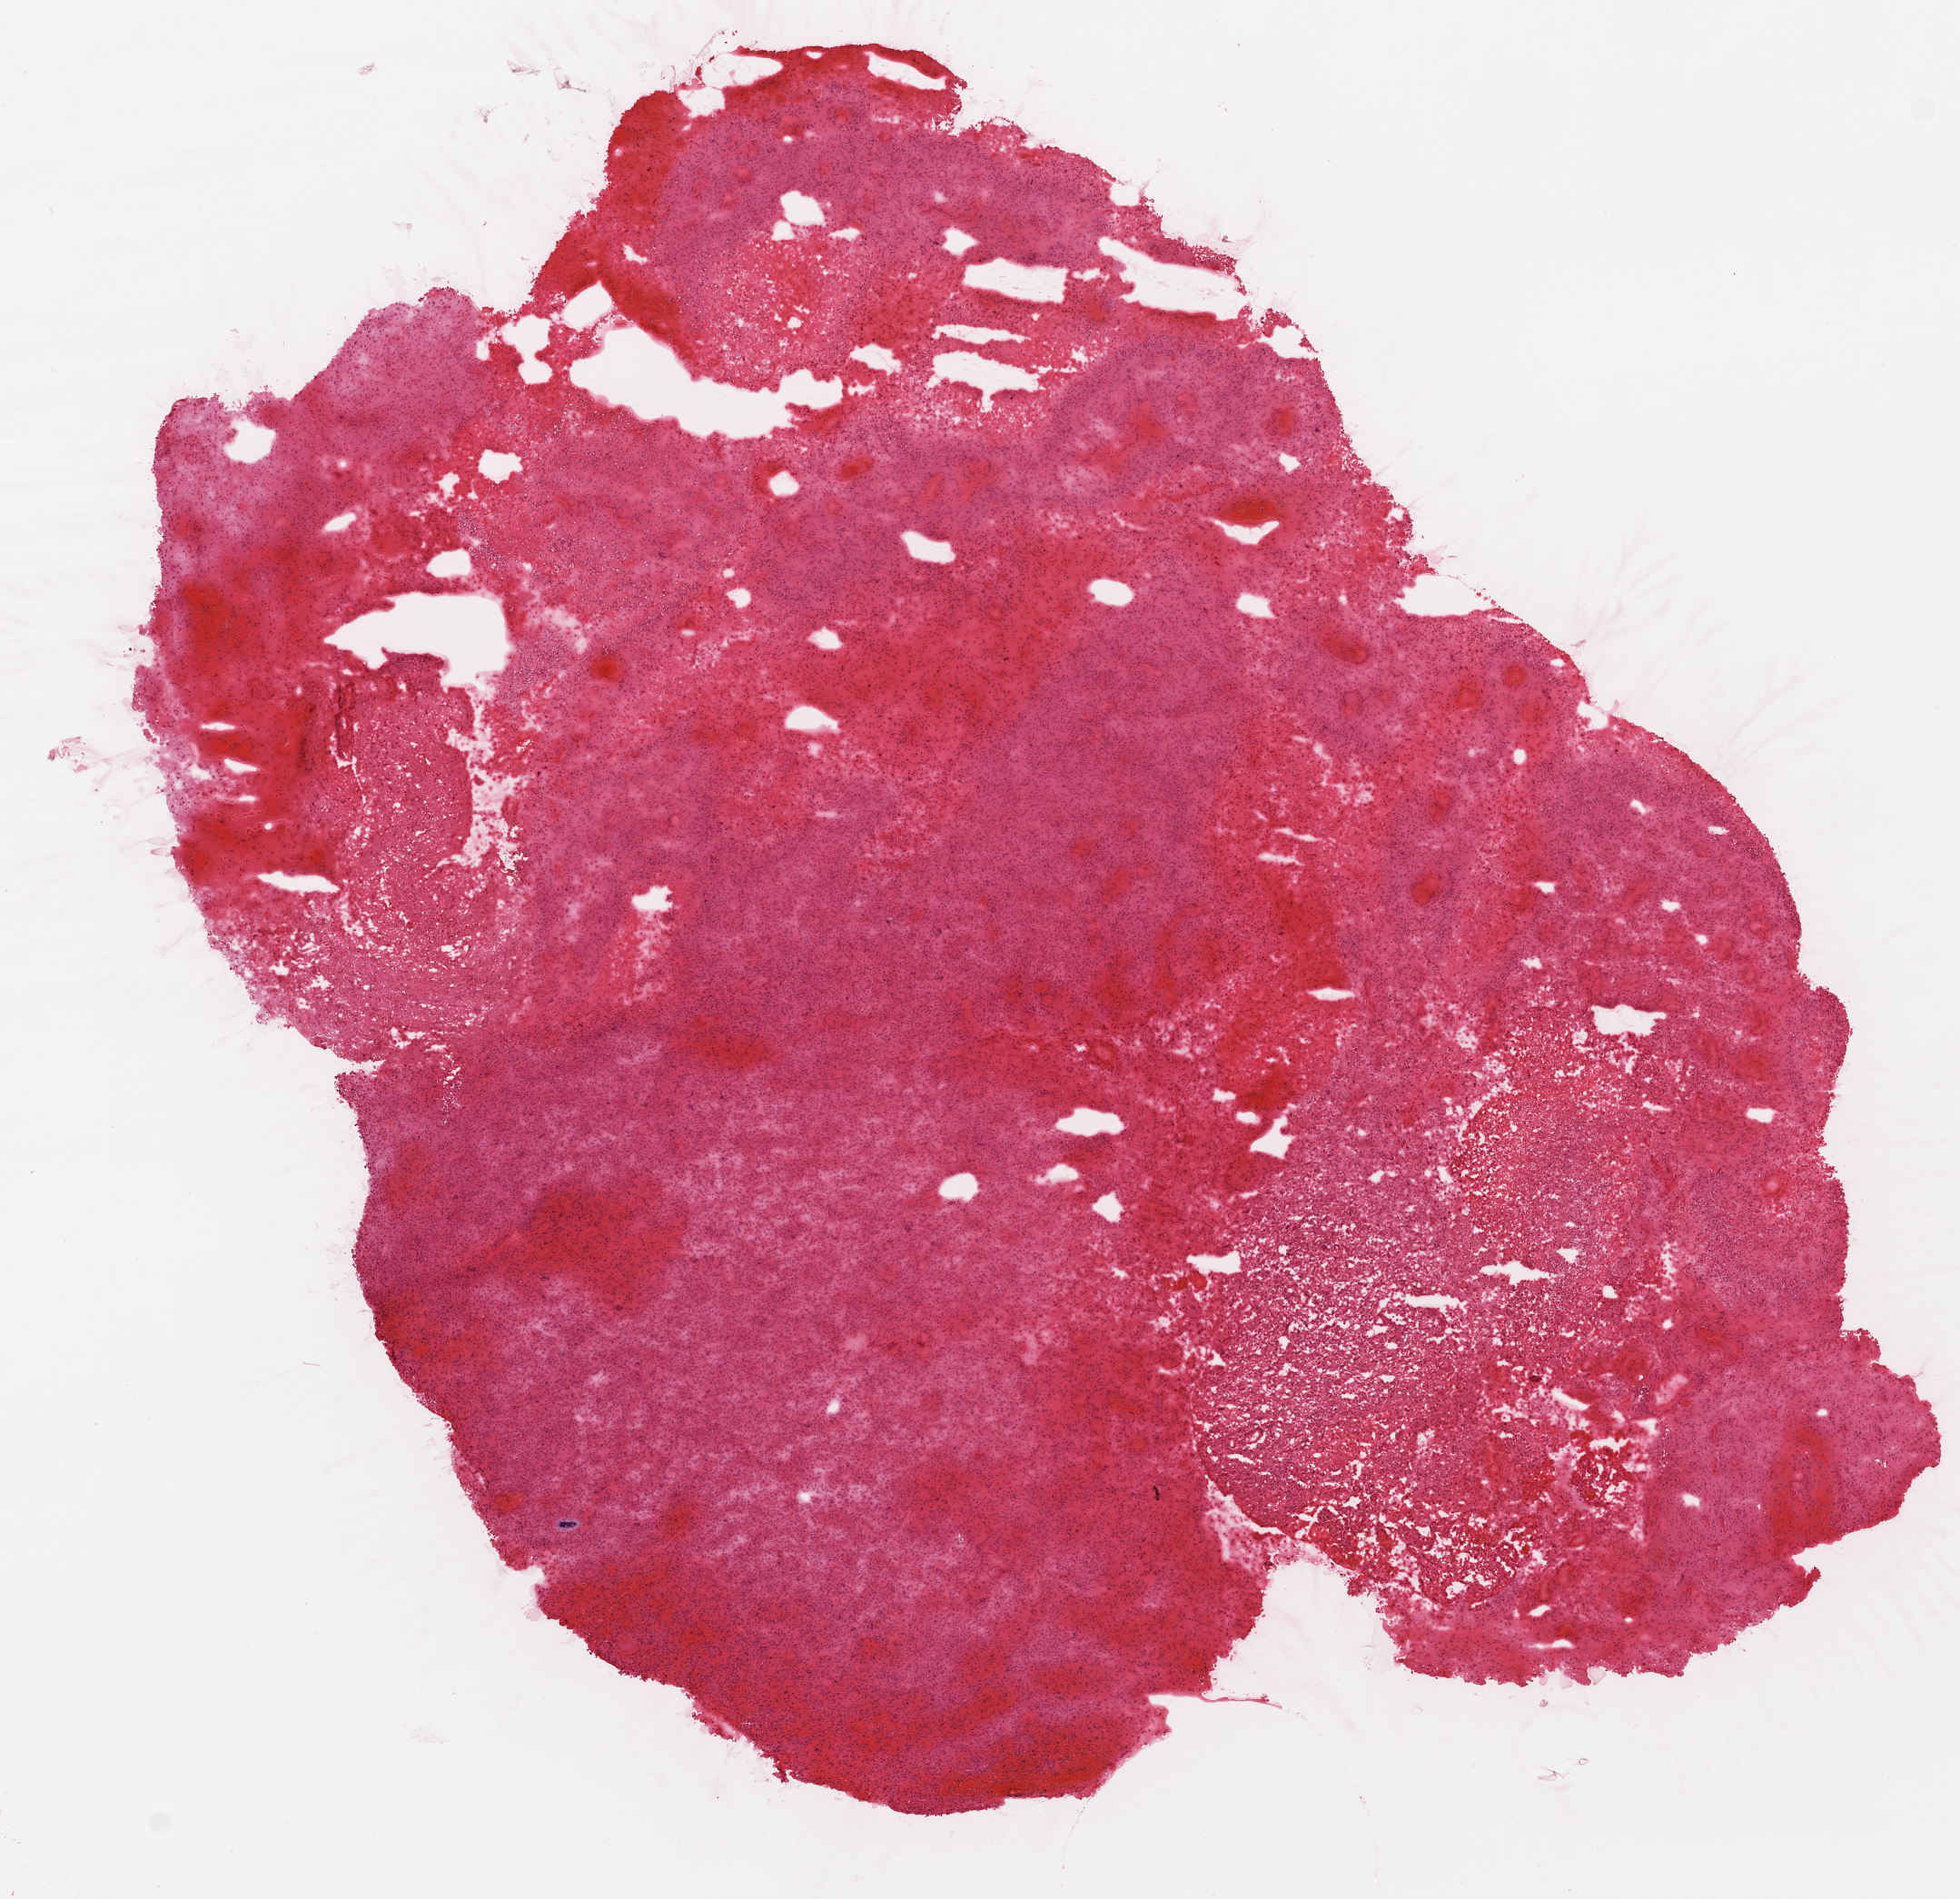
Digitized Hematoxylin and eosin (H&E) stained tissue section (whole slide), a low-resolution overview of the entire scanned area, about 8.7 x 8.4 mm, frozen section from the top of the tissue portion, brain, primary tumour sample. Male patient; age at initial diagnosis 52 years. Composition of this section per pathologist review: tumour cells 70%, tumour nuclei 90%, normal cells 0%, stromal cells 0%, necrosis 30%.
- pathologic diagnosis: Glioblastoma